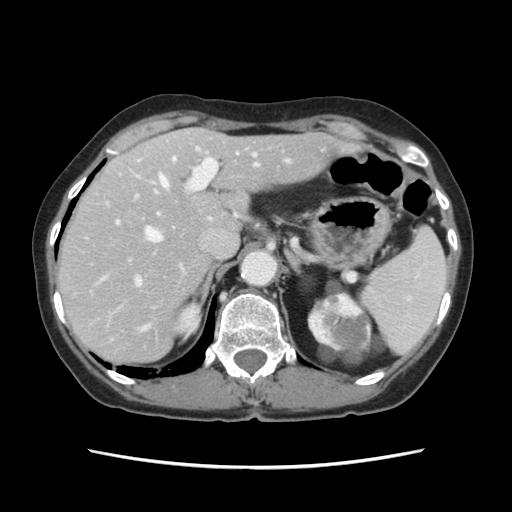
Contrast-enhanced abdominal CT, one axial slice. Slice 85 of 120 in the series (ordered by position). Intravenous contrast given. Soft-tissue window (W 400 / L 40 HU). 512 × 512 image matrix, field of view 330 × 330 mm. Female patient, age 70 years. From the clinical record (not read from this slice): diagnosis: colorectal cancer liver metastases, imaged before liver resection; multiple liver metastases: no; largest metastasis: 2.5 cm.
Annotated regions visible in this slice (manually delineated by an expert):
- hepatic veins: bounding box (x1, y1, x2, y2) in pixels: (145, 153, 259, 326)
- liver: (59, 128, 345, 362)
- planned liver remnant (the part of the liver to remain after resection): (106, 128, 344, 291)
- portal vein (with intrahepatic branches): (101, 147, 290, 286)